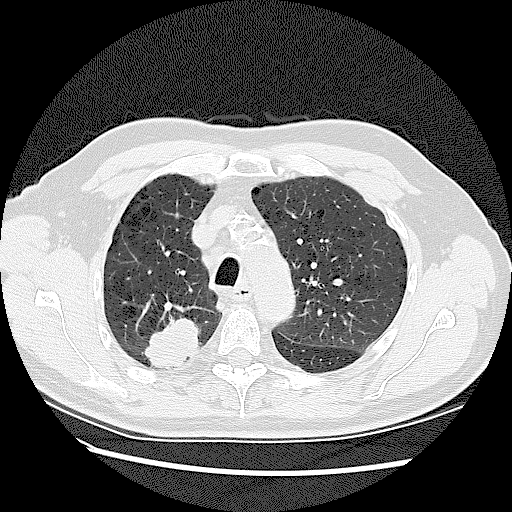
Chest CT (low-dose screening protocol), one axial image, first (baseline) screen, lung window (W 1500 / L -600 HU). Male, age 72 years at enrolment. Current smoker at enrolment.
• Lesion marked by an expert reader, bounding box <138,310,213,376> (left, top, right, bottom; pixels).
• The screening reader recorded 2 non-calcified nodules or masses ≥4 mm on this exam (right upper lobe, right upper lobe); which of them this box marks is not recorded.
• Official screen result: positive, change unspecified: nodule(s) >= 4 mm or enlarging nodule(s), mass(es), or other non-specific abnormalities suspicious for lung cancer.
• Later outcome: lung cancer diagnosed 42 days after this screen — adenocarcinoma, NOS, right upper lobe, stage IV (AJCC 6th edition), 45 mm at pathology.